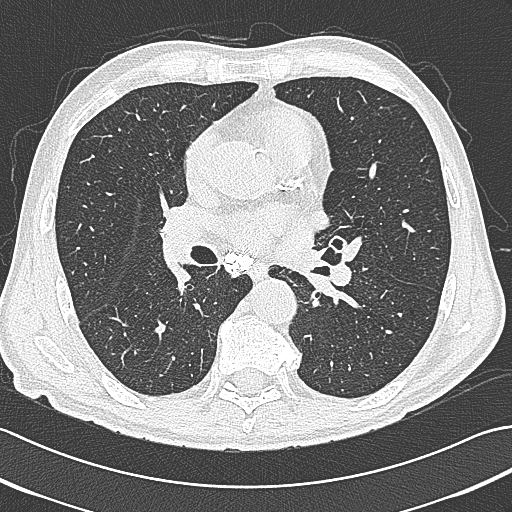
Chest CT (low-dose screening protocol), one axial image; baseline annual screen; lung window (W 1500 / L -600 HU). Male participant, aged 65 years at enrolment.
• Lesion marked by an expert reader, box from (x=305, y=233) to (x=356, y=272) px.
• Screening reader's record for this exam: no non-calcified nodule ≥4 mm recorded.
• Official screen result: negative screen, minor abnormalities not suspicious for lung cancer.
• Lung cancer was diagnosed 161 days after this screen: large cell neuroendocrine carcinoma, left hilum, left main stem bronchus, stage IIIB (AJCC 6th edition), 70 mm at pathology.